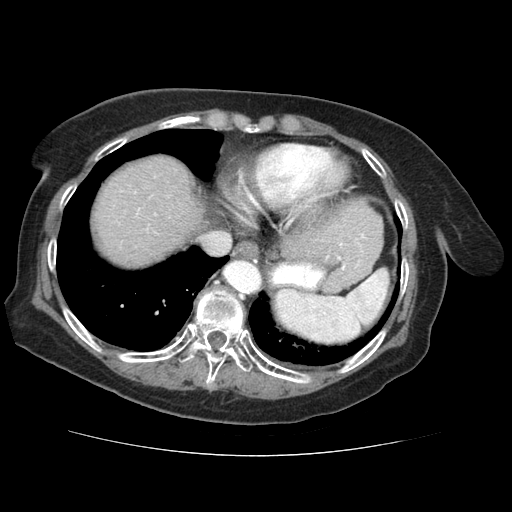
Contrast-enhanced abdominal CT (liver protocol), one axial slice; position 57 of 73 along the scan axis; reconstruction kernel STANDARD; 120 kVp; soft-tissue window (W 400 / L 40 HU); 2.5 mm slice thickness; 512 × 512 image matrix, field of view 360 × 360 mm. Case-level facts recorded for this patient, not image findings: diagnosis: hepatocellular carcinoma (patient treated with transarterial chemoembolisation; whether this scan precedes or follows treatment is not stated here); TNM stage (as recorded): Stage-IVB.
Annotated regions visible in this slice (semi-automatically segmented with operator editing):
- liver parenchyma outside the tumour (the mass and vessels are separate outlines, so this box may not span the whole liver): bounding box (x1, y1, x2, y2) in pixels: (94, 156, 202, 264)